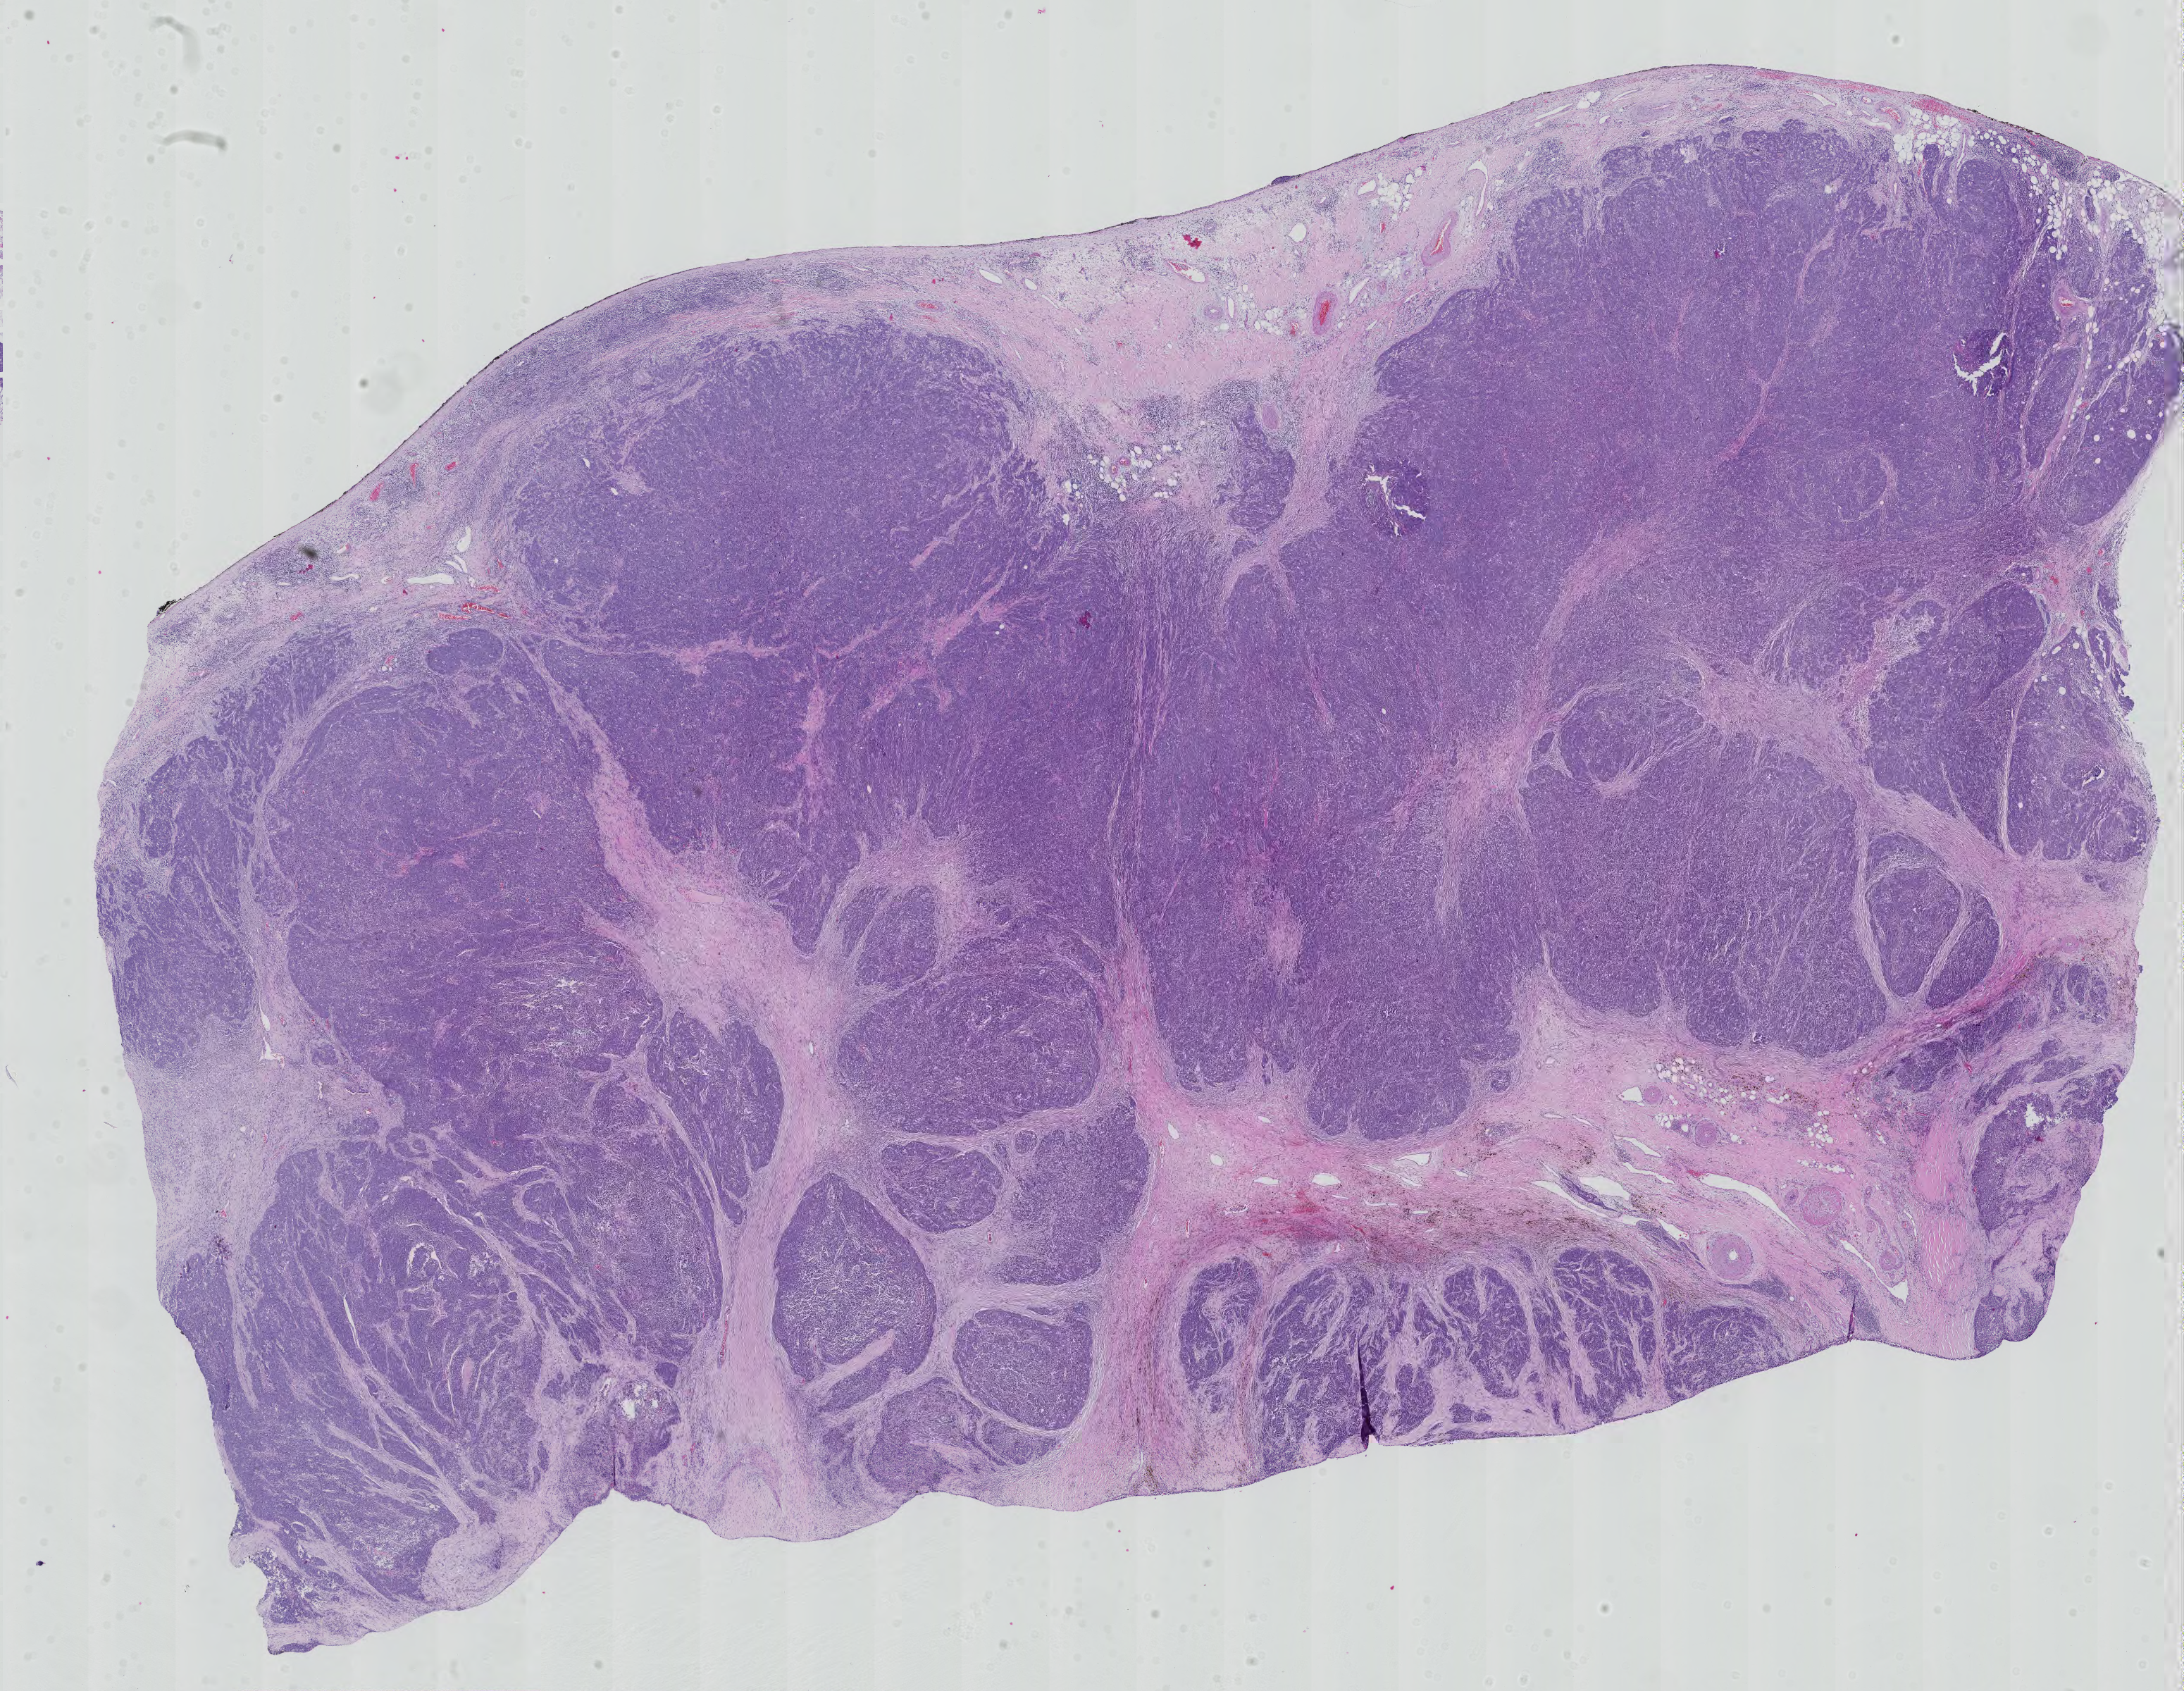
Hematoxylin and eosin (H&E) stained whole-slide image, low-resolution overview of the scanned area, about 22.6 x 17.5 mm, formalin-fixed paraffin-embedded (FFPE) diagnostic section, sample: primary tumour, thymus. Male patient; age at initial diagnosis 44 years.
Pathologic diagnosis: Thymic carcinoma, NOS.